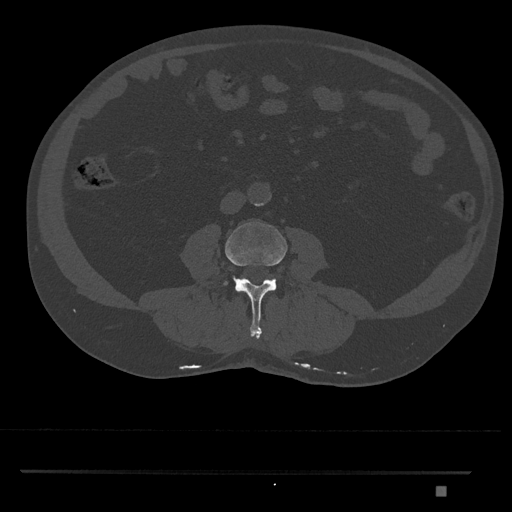
CT including the spine, one axial slice. Position 672 of 1134 along the scan axis. 120 kVp. Bone window (W 1800 / L 400 HU). 0.5 mm slice thickness. 512 × 512 image matrix, field of view 429 × 429 mm. Patient: male, 65 years. Case-level facts recorded for this patient, not image findings: primary cancer: prostate.
Structures marked on this image (semi-automatically segmented with operator editing):
- L3 vertebra: bounding box (x1, y1, x2, y2) in pixels: (223, 222, 294, 339)